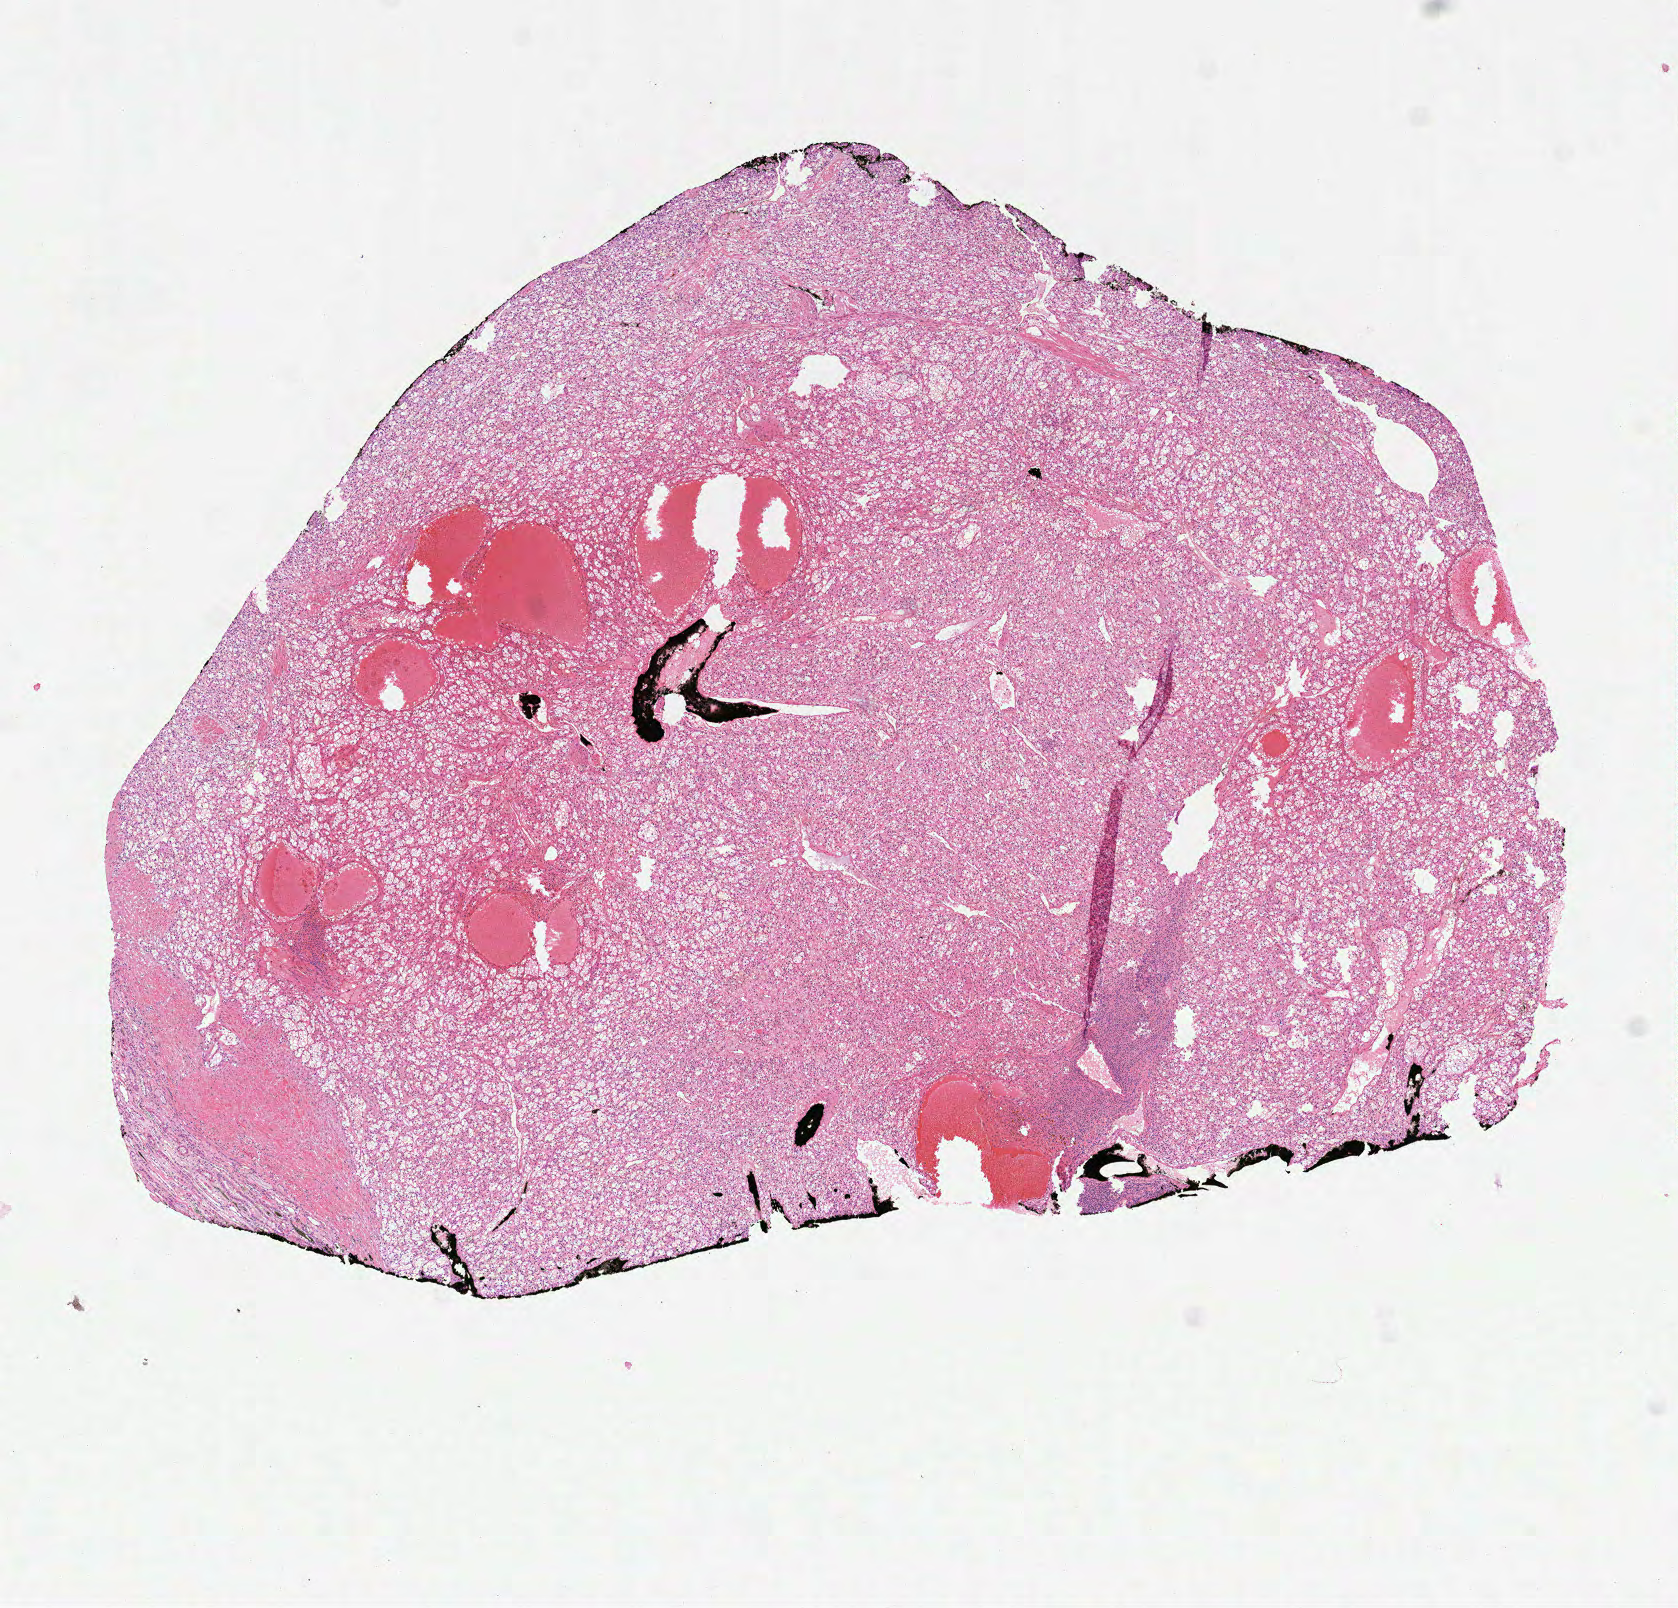
H&E-stained whole-slide image, low-resolution overview of the scanned area, about 6.8 x 6.5 mm (from a 40x scan); FFPE section; primary tumour sample from the kidney. Patient: male, age at initial diagnosis 46 years. Histologic grade: G2 (moderately differentiated).
- AJCC pathologic stage: I
- pathologic diagnosis: Clear cell adenocarcinoma, NOS